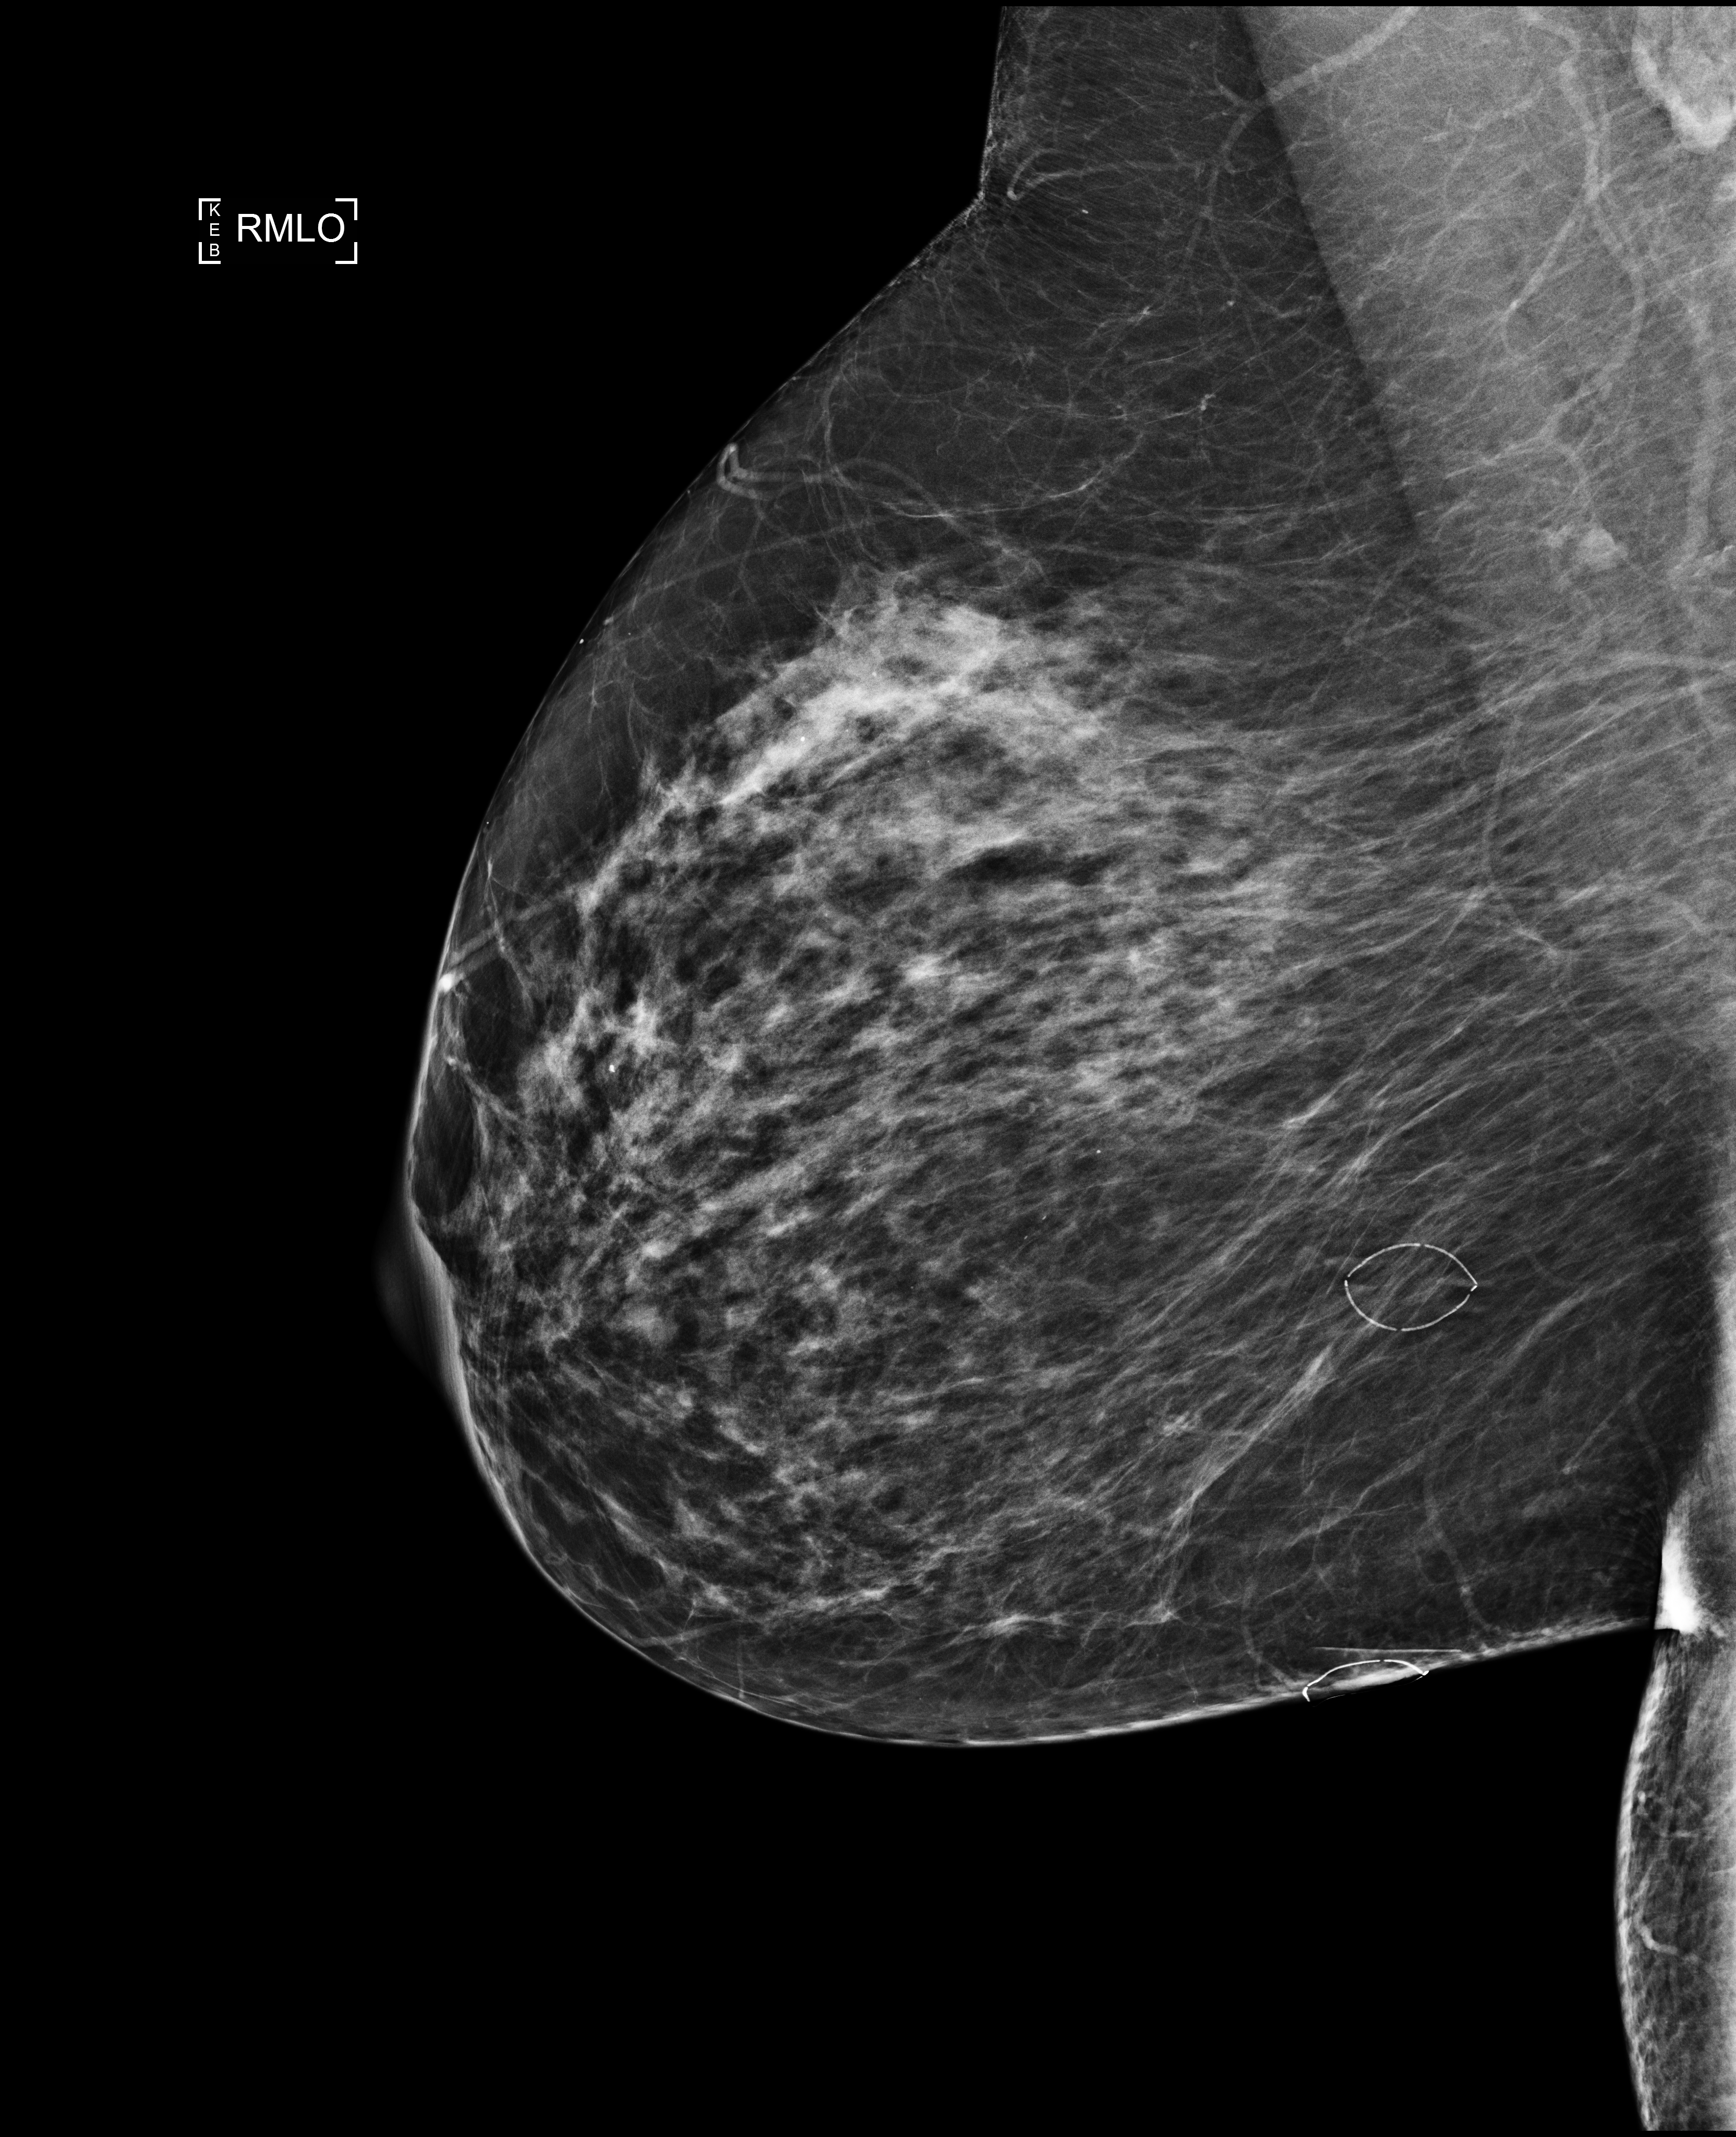
Annual screening mammography examination; compressed breast thickness 69 mm. Female patient, age 62 years.
Image type: full-field digital mammogram. Breast: right. Projection: mediolateral oblique (MLO) view.